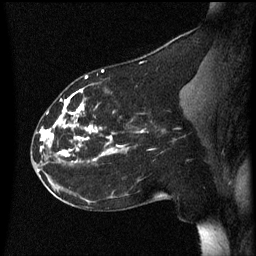
Breast MRI (dynamic contrast-enhanced), one sagittal slice. Slice 26 of 60 in the series (ordered by position). Dynamic contrast-enhanced series, image 2 of 3 at this slice position (ordered by acquisition). 1.5 T. TE 4.2 ms, TR 8.4 ms. 2.2 mm slice thickness. 256 × 256 image matrix, field of view 200 × 200 mm. Patient: female, 35 years. From the clinical record (not read from this slice): setting: breast cancer imaged before/during neoadjuvant chemotherapy; receptor status: HER2-positive.
Outlined on this slice (semi-automatic segmentation, software-assisted and operator-edited):
- analysis volume of interest (the breast-tissue region the enhancement analysis was run in; not a lesion): box from (x=32, y=72) to (x=177, y=173) px
- tumour enhancement mask (voxels above the 70 % enhancement threshold inside the analysis volume of interest): (x=40, y=72)–(x=129, y=163)